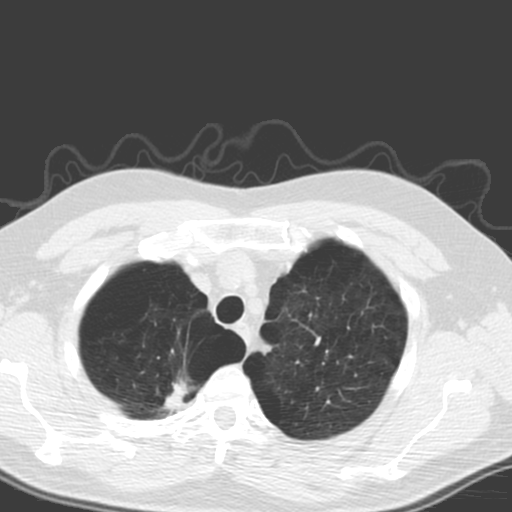
Axial slice from a low-dose chest CT screening exam. Baseline screening round. Lung window (W 1500 / L -600 HU). Standard (soft-tissue) reconstruction kernel (B). Slice 30 of 173 in the series. 512 × 512 image matrix, field of view 340 × 340 mm. Male participant, aged 56 years at enrolment.
• Expert-annotated lung lesion, box from (x=138, y=354) to (x=209, y=425) px.
• Reader record for this screening exam (exam-level; its link to the box is not recorded): non-calcified nodule or mass ≥4 mm, right upper lobe, 20 × 12 mm, spiculated (stellate) margins, soft tissue attenuation.
• Official screen result: positive, change unspecified: nodule(s) >= 4 mm or enlarging nodule(s), mass(es), or other non-specific abnormalities suspicious for lung cancer.
• Participant outcome: lung cancer diagnosed 205 days after this screen — large cell carcinoma, NOS, right upper lobe, poorly differentiated (G3), stage IA (AJCC 6th edition), 18 mm at pathology.